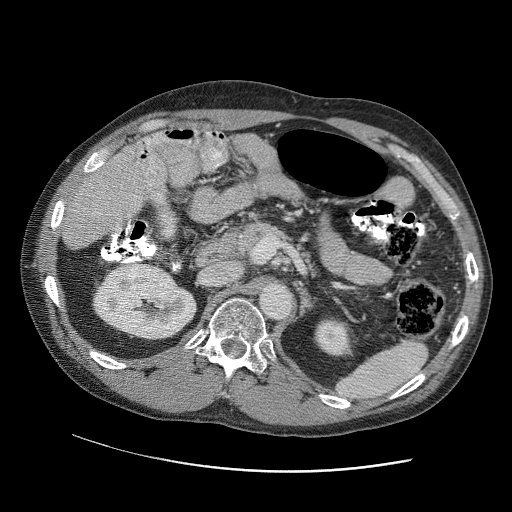
Contrast-enhanced abdominal CT (liver protocol), one axial slice. Position 53 of 109 along the scan axis. Soft-tissue window (W 400 / L 40 HU). 2.5 mm slice thickness. 512 × 512 image matrix, field of view 400 × 400 mm. Case-level facts recorded for this patient, not image findings: diagnosis: hepatocellular carcinoma (patient treated with transarterial chemoembolisation; whether this scan precedes or follows treatment is not stated here); TNM stage (as recorded): Stage-IIIC; Child-Pugh class: B.
Outlined on this slice (semi-automatically segmented with operator editing):
- liver parenchyma outside the tumour (the mass and vessels are separate outlines, so this box may not span the whole liver): bounding box <107,141,163,170> (left, top, right, bottom; pixels)
- liver vessels: <124,142,160,162>